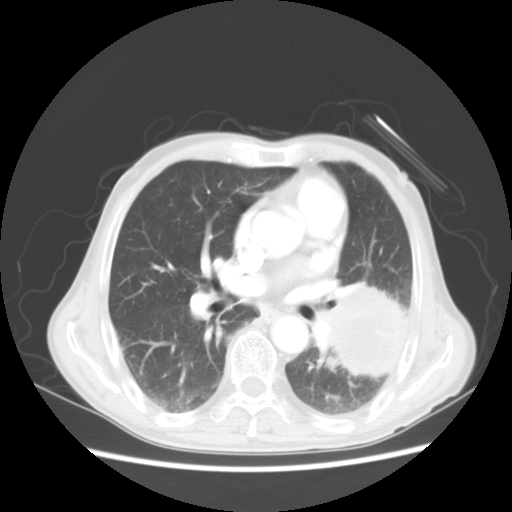
Chest CT, one axial slice; position 26 of 51 along the scan axis; reconstruction kernel STANDARD; lung window (W 1500 / L -600 HU); 5 mm slice thickness; 512 × 512 image matrix, field of view 360 × 360 mm. Male patient, age 64 years. From the clinical record (not read from this slice): clinical TNM (as recorded): T4 N0 M0.
Annotated regions visible in this slice (rectangle marked by the reading radiologist):
- lung tumour (recorded histology: squamous cell carcinoma): bounding box <327,289,422,380> (left, top, right, bottom; pixels)